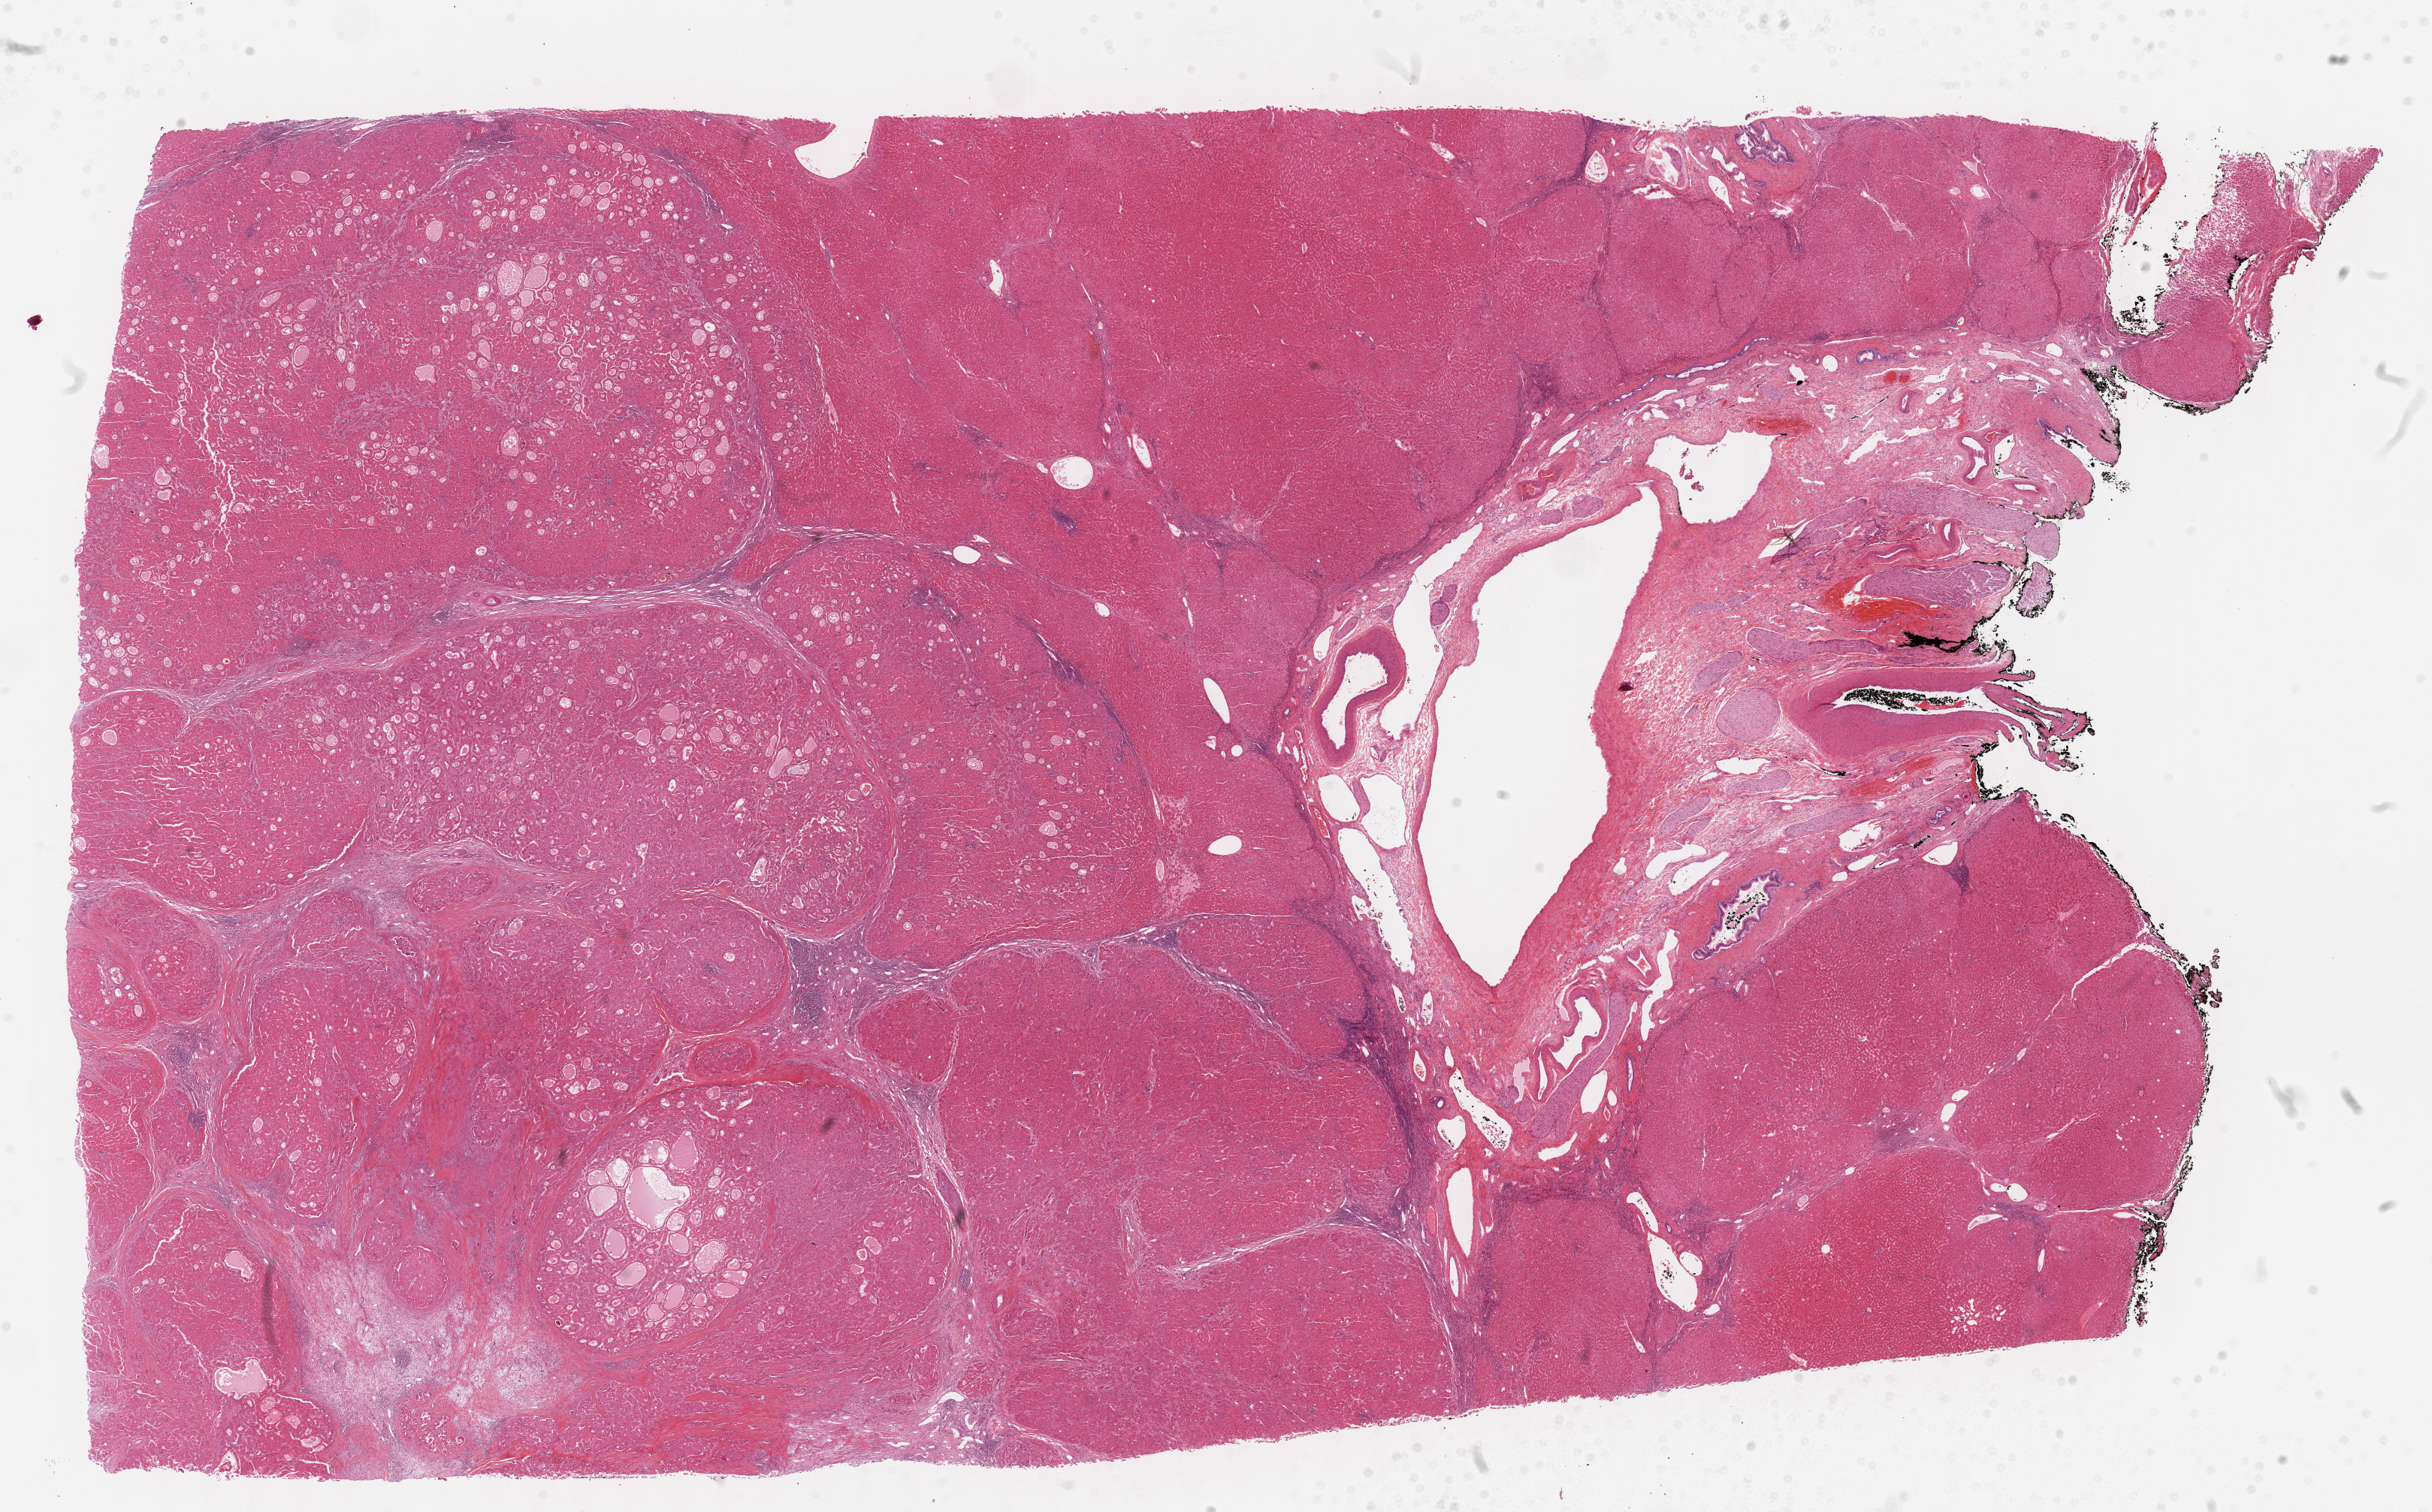
Whole-slide histology image, H&E-stained, a low-resolution overview of the entire scanned area, about 26.2 x 16.3 mm; formalin-fixed paraffin-embedded (FFPE) diagnostic section; liver, primary tumour sample. Male, age 51 years at initial diagnosis. Histologic grade: G2 (moderately differentiated).
Pathologic diagnosis: Hepatocellular carcinoma, NOS. AJCC pathologic stage: I (6th edition).